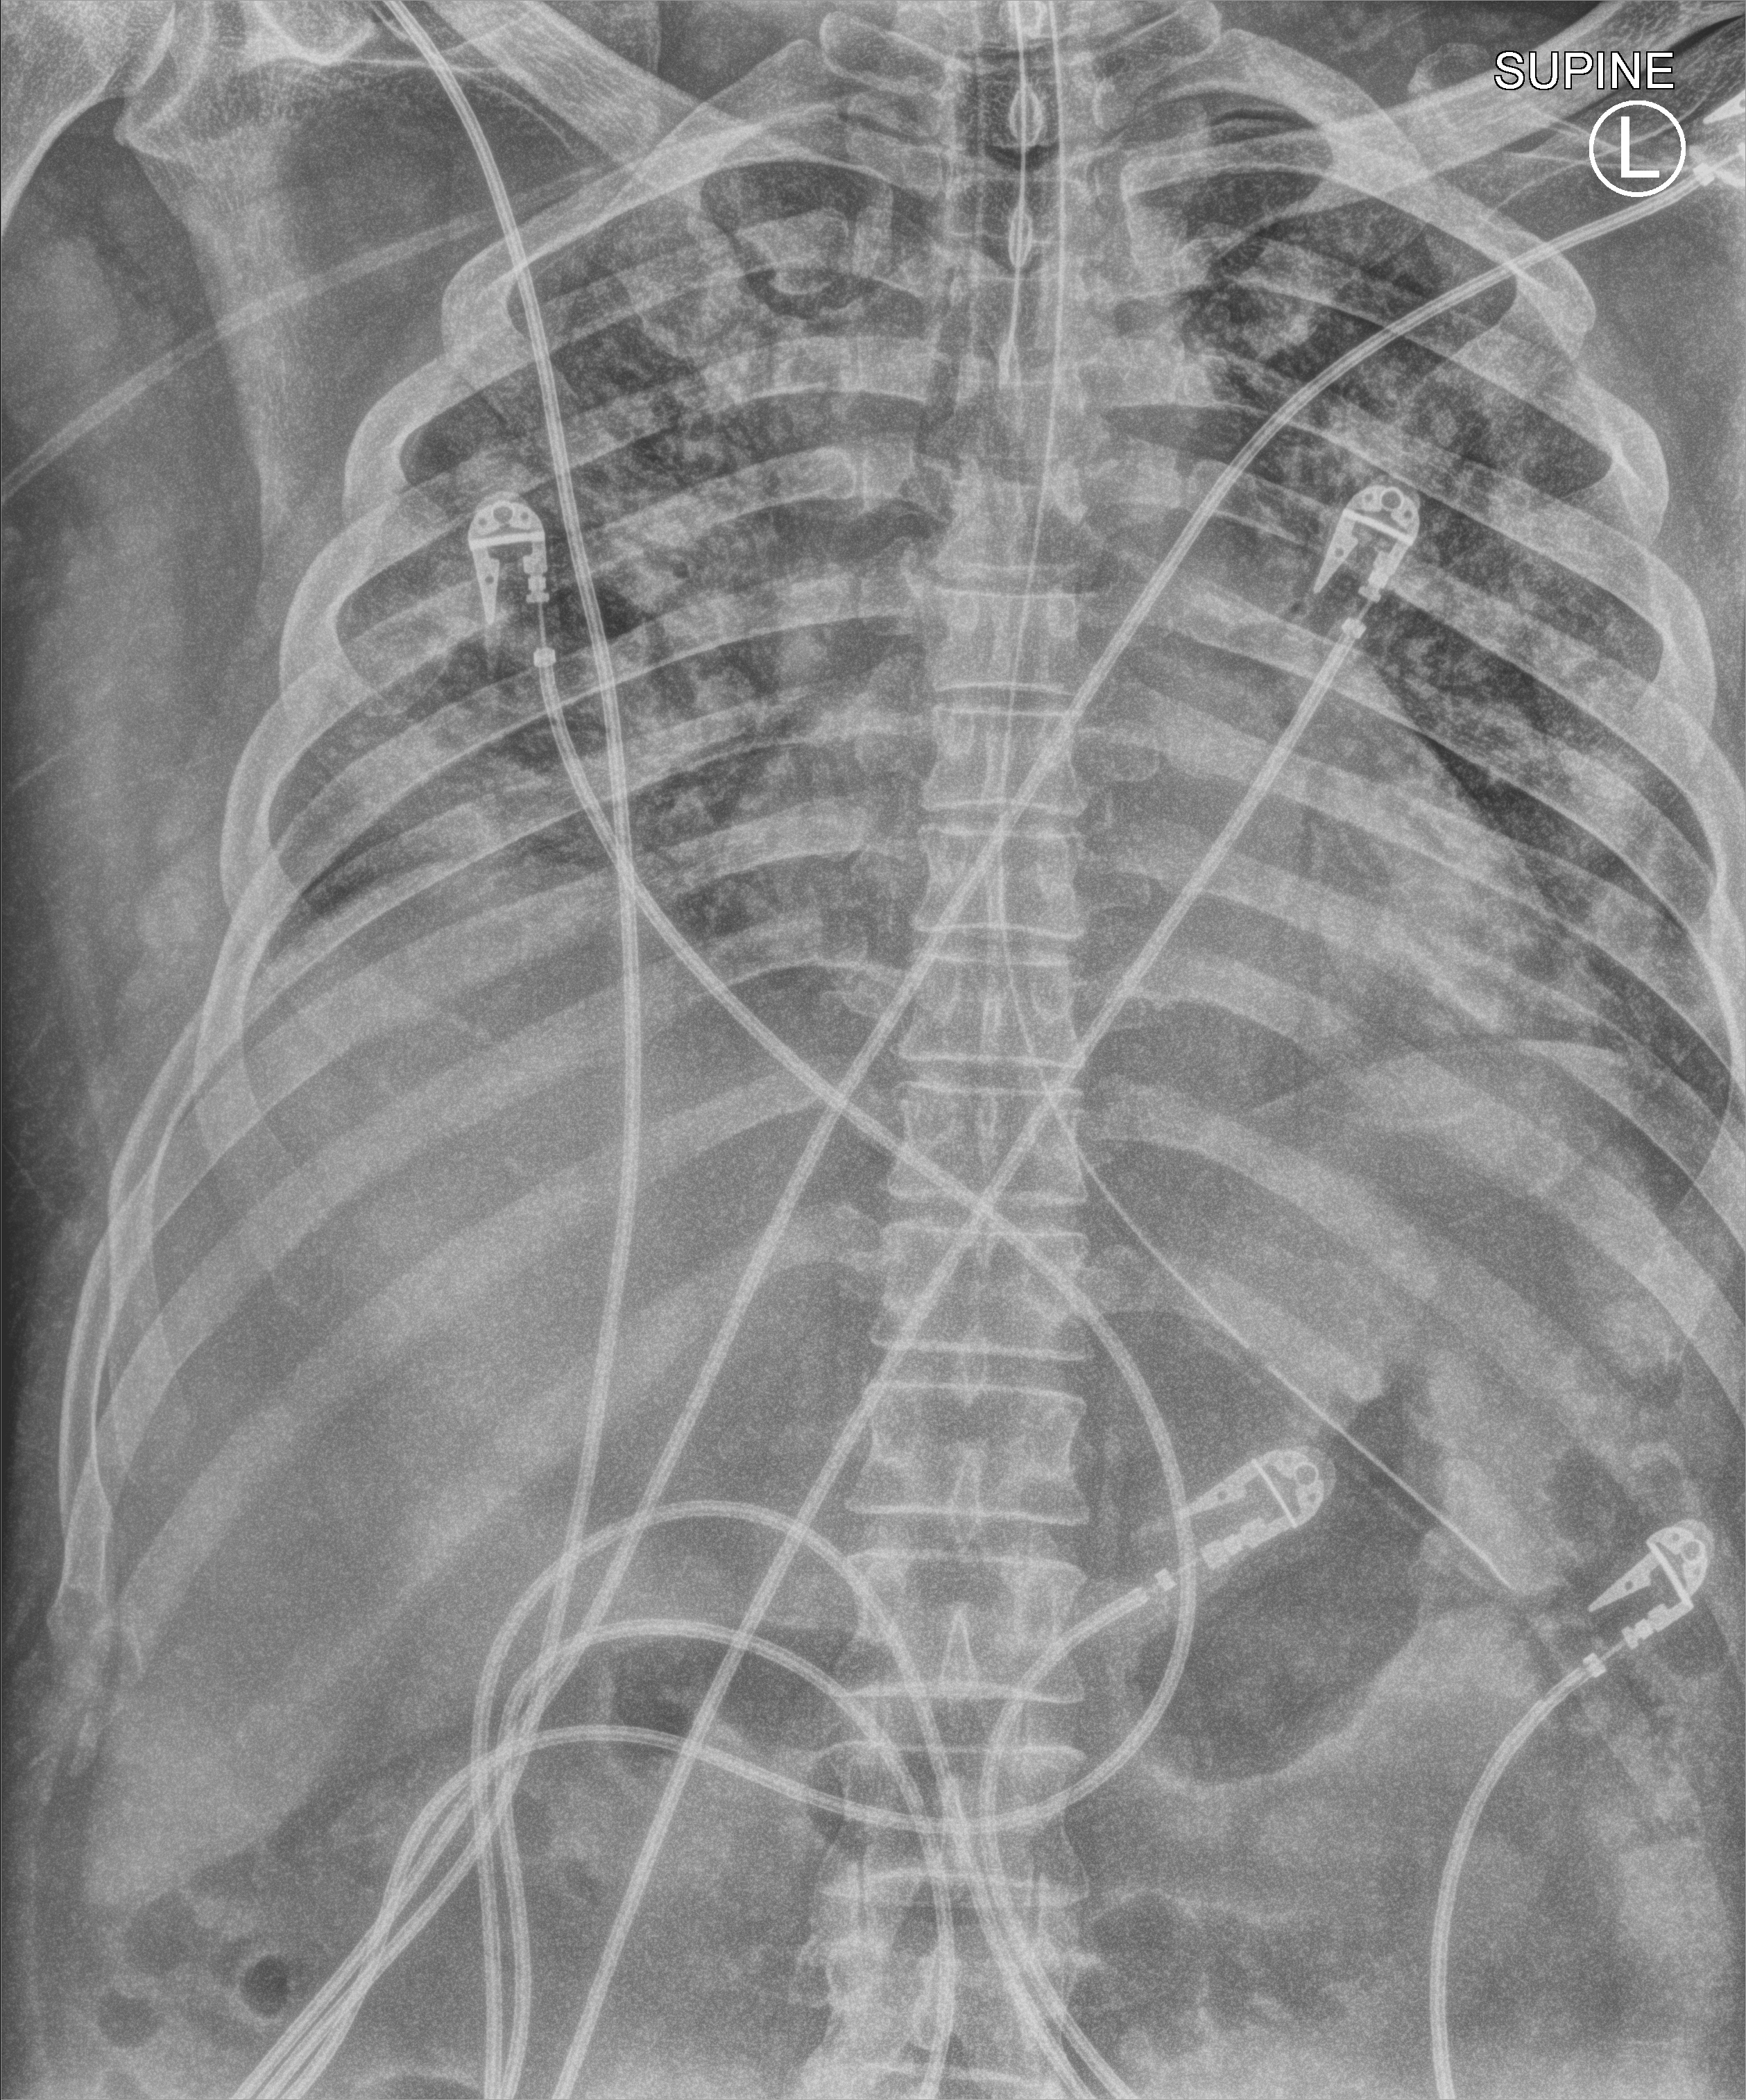
Portable chest radiograph; anteroposterior (AP) projection. Patient hospitalised with COVID-19; male, aged 18–59 years.
From the hospital-stay record, not from the radiograph (when in the stay this image was taken is not recorded):
- mechanically ventilated during this hospital stay: yes